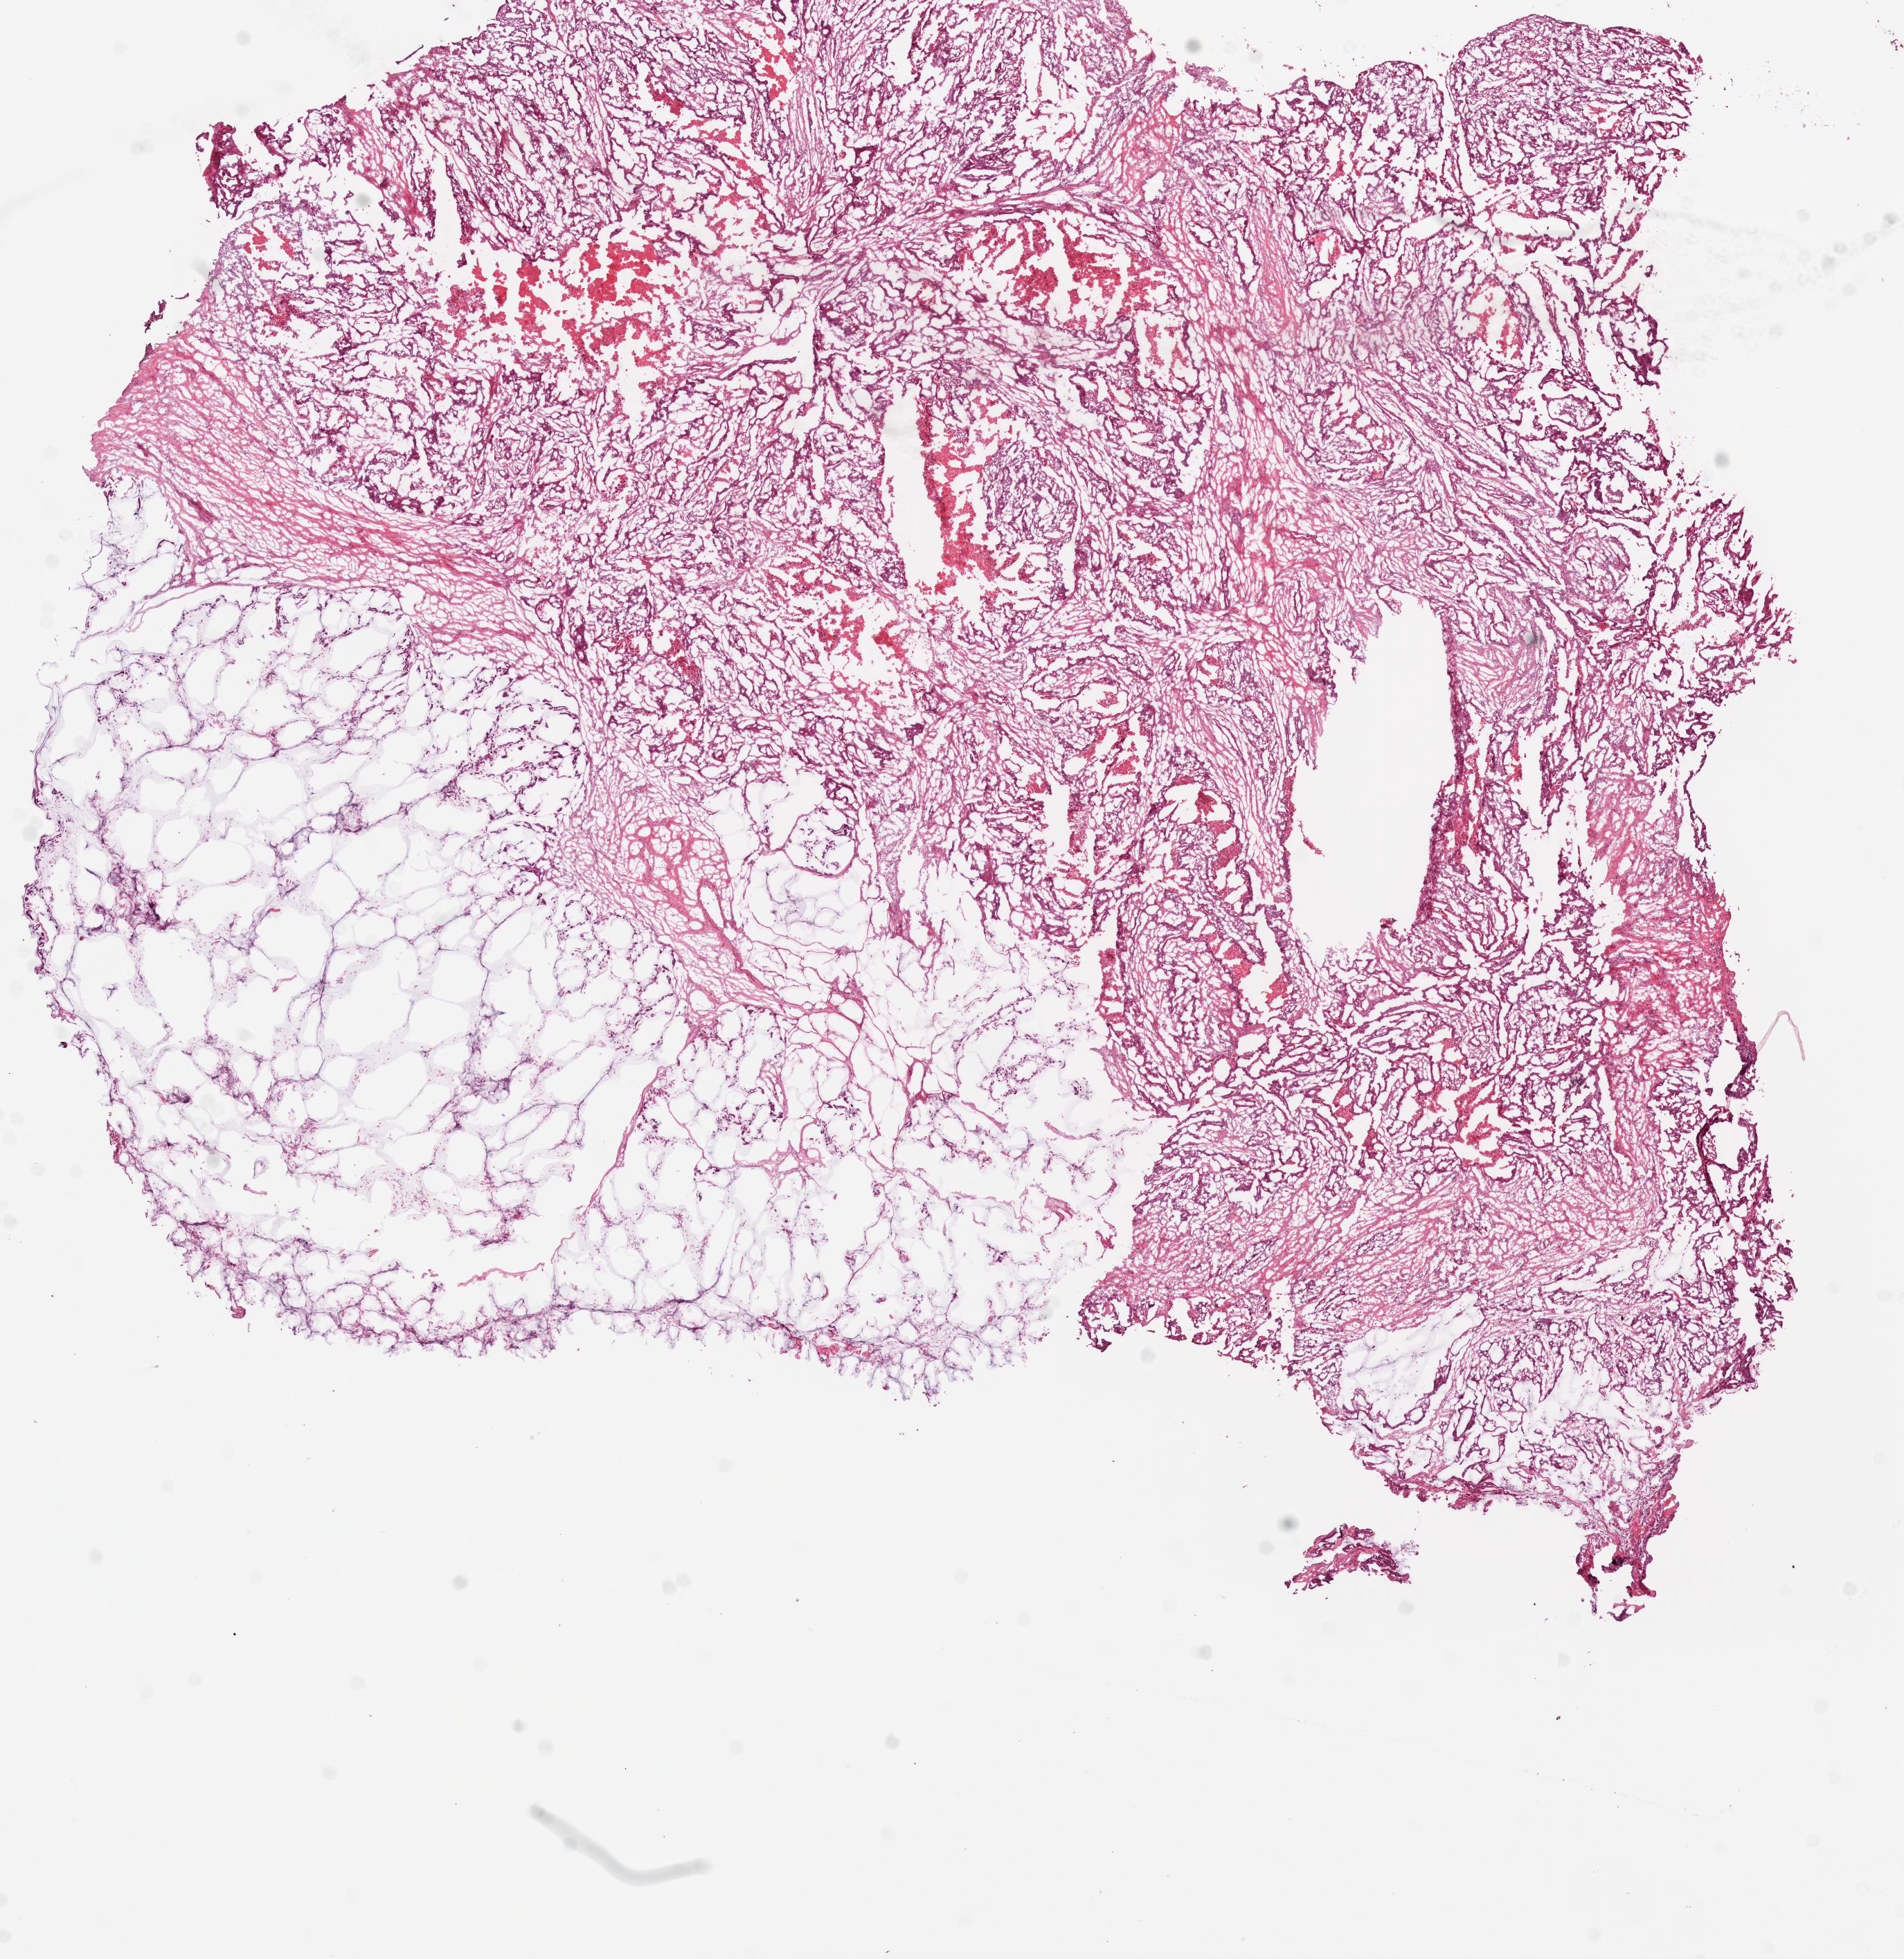
Whole-slide histology image, Hematoxylin and eosin (H&E) stained, low-resolution overview of the scanned area, about 11.0 x 11.4 mm, frozen section from the bottom of the tissue portion, sample: primary tumour, colon. Male patient; age at initial diagnosis 84 years. Pathologist review of this section (percent, as recorded): tumour cells 75%, tumour nuclei 75%.
Diagnosis: Adenocarcinoma, NOS.